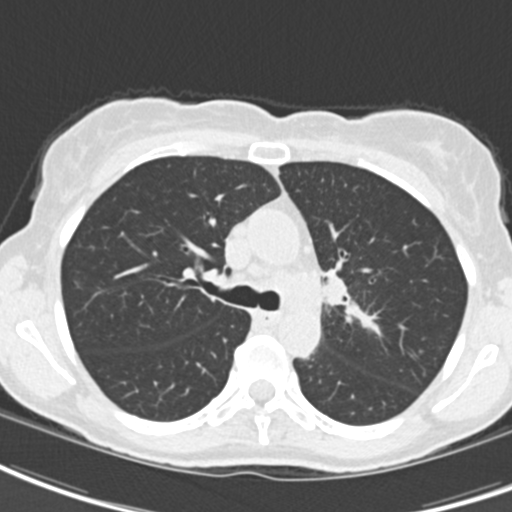
Chest CT (low-dose screening protocol), one axial image, first (baseline) screen, lung window (W 1500 / L -600 HU), 2 mm slice thickness, 512 × 512 image matrix, field of view 279 × 279 mm. Female participant, aged 62 years at enrolment. Current smoker at enrolment.
• Expert reader's lesion annotation, box from (x=293, y=252) to (x=366, y=336) px.
• Reader record for this screening exam (exam-level; its link to the box is not recorded): non-calcified nodule or mass ≥4 mm, right upper lobe, 24 × 20 mm, smooth margins, ground glass attenuation.
• Note: the box lies in the patient's left hemithorax on this image, whereas the reader's record names the right lung; they may be different findings.
• Official screen result: positive, change unspecified: nodule(s) >= 4 mm or enlarging nodule(s), mass(es), or other non-specific abnormalities suspicious for lung cancer.